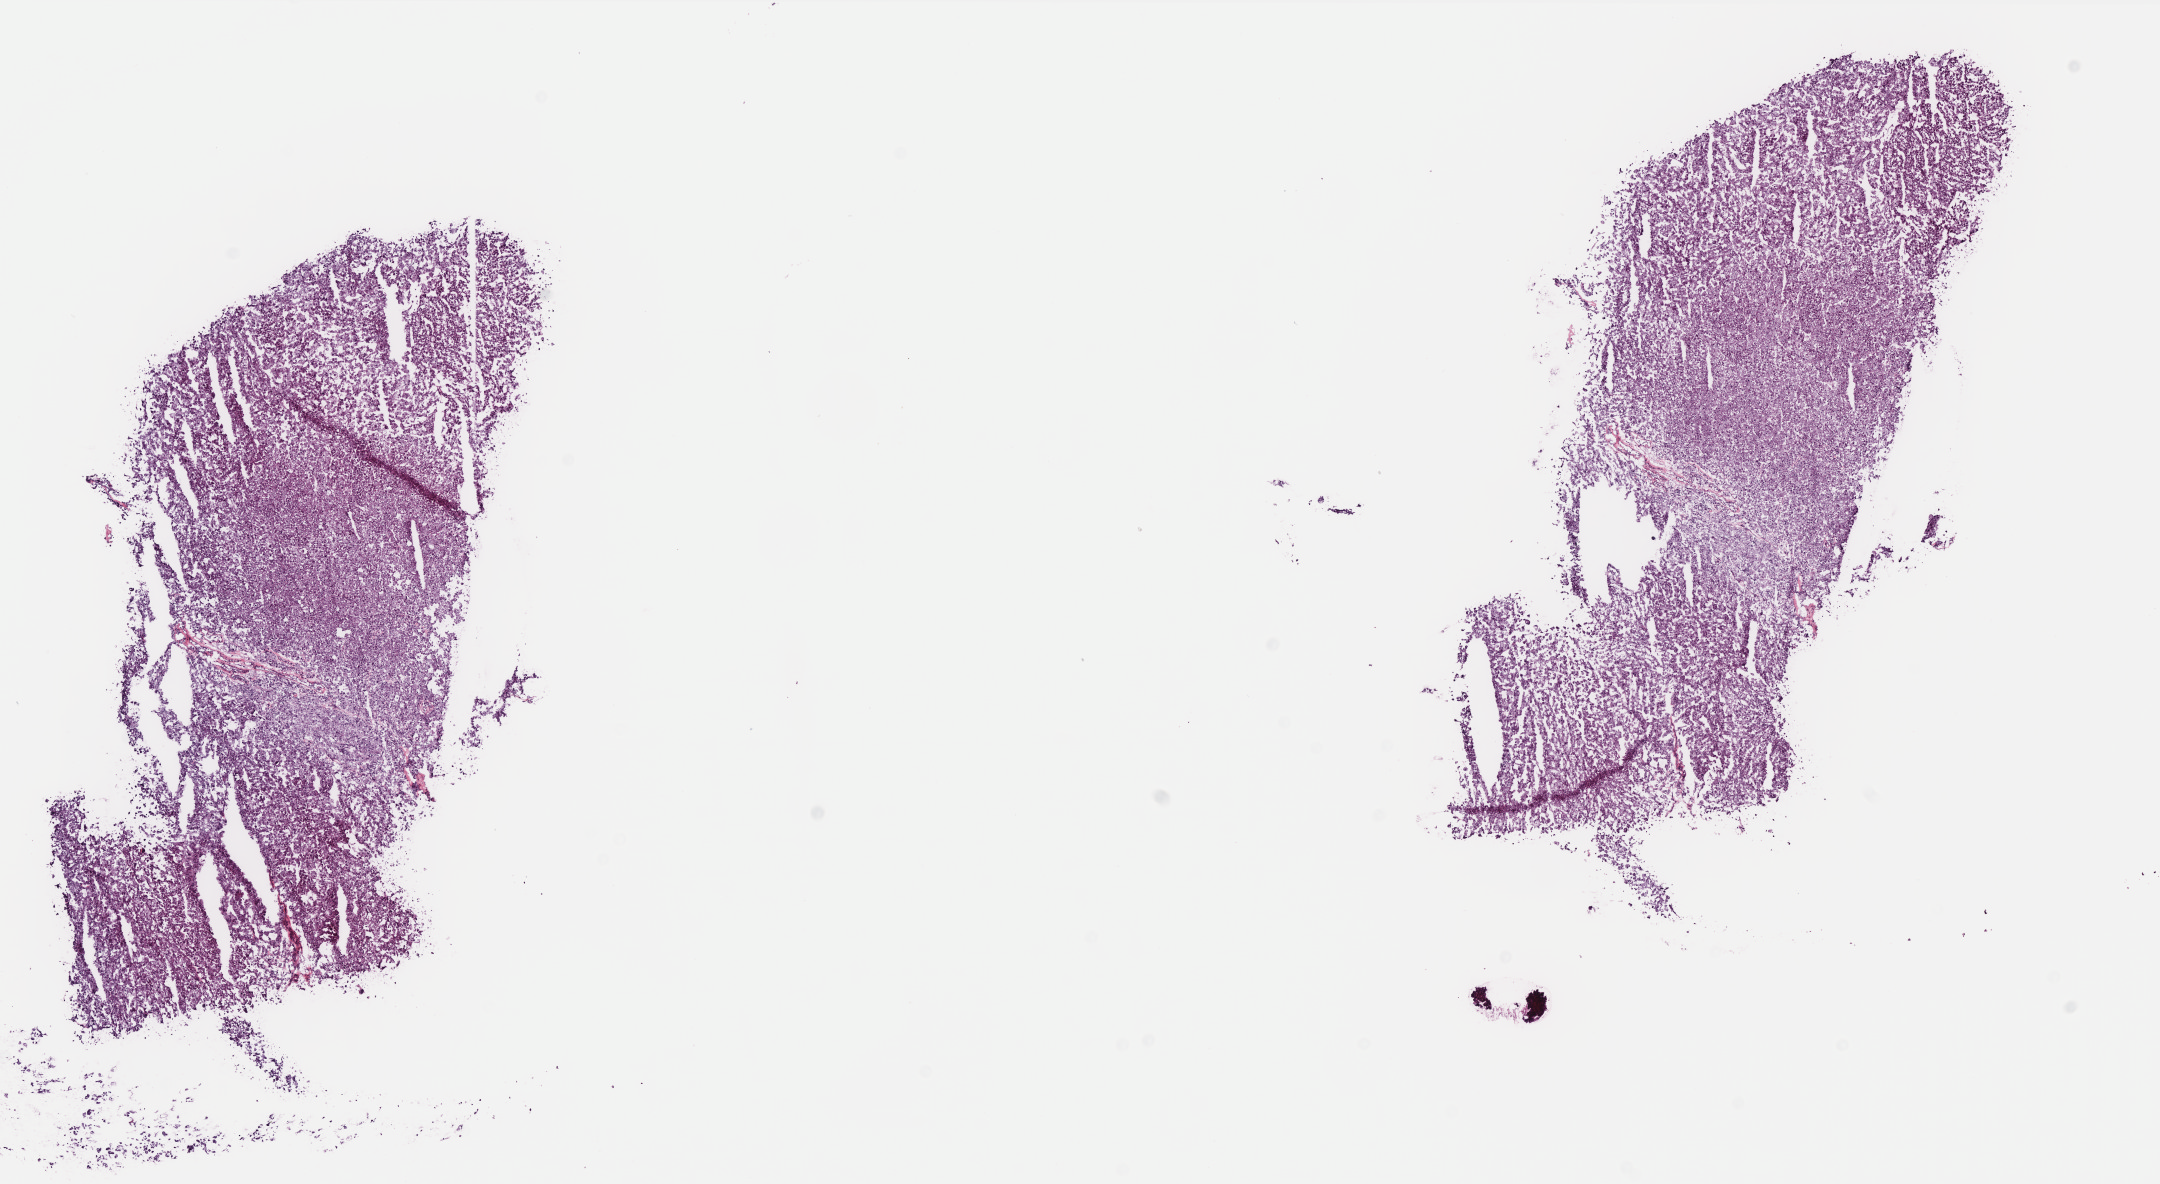
Digitized H&E tissue section (whole slide) — shown as a low-resolution overview of the whole scanned area (about 17.3 x 9.5 mm, acquisition: 40x scan). Frozen section. Sample: primary tumour, kidney. Female, age 29 years at initial diagnosis. Composition of this section per pathologist review: tumour cells 90%, tumour nuclei 95%, normal cells 0%, stromal cells 0%, necrosis 10%. Inflammatory infiltration, as recorded: lymphocyte infiltration 0%, monocyte infiltration 0%, neutrophil infiltration 0%.
Lymph nodes positive (case pathology): 0 of 7 examined. AJCC pathologic stage: I (7th edition). Pathologic diagnosis: Renal cell carcinoma, chromophobe type.